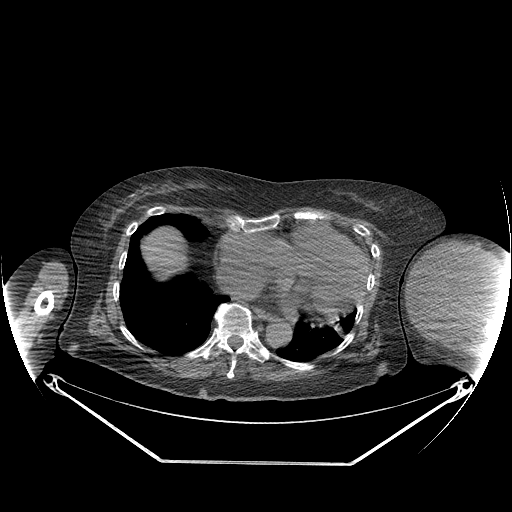
CT of an extremity soft-tissue mass (from a PET/CT study), one axial slice. Position 154 of 267 along the scan axis. Reconstruction kernel STANDARD. 140 kVp. Soft-tissue window (W 400 / L 40 HU). 3.75 mm slice thickness. 512 × 512 image matrix. Female patient. Case-level facts recorded for this patient, not image findings: histological type: pleiomorphic leiomyosarcoma; grade: high; site of the primary tumour: left biceps.
Annotated regions visible in this slice (expert contour drawn on MRI and transferred to this co-registered scan by the dataset authors):
- gross tumour volume including surrounding oedema: bounding box <407,242,497,330> (left, top, right, bottom; pixels)
- gross tumour volume (mass): <407,242,497,328>